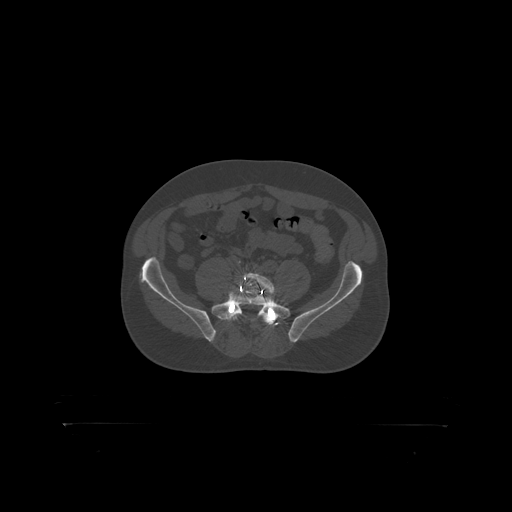
CT including the spine, one axial slice; slice 191 of 399 in the series (ordered by position); 120 kVp; bone window (W 1800 / L 400 HU); 1.25 mm slice thickness; 512 × 512 image matrix, field of view 650 × 650 mm. Male patient, age 46 years. From the clinical record (not read from this slice): primary cancer: skin.
Structures marked on this image (semi-automatically segmented with operator editing):
- L5 vertebra: box from (x=241, y=274) to (x=275, y=296) px